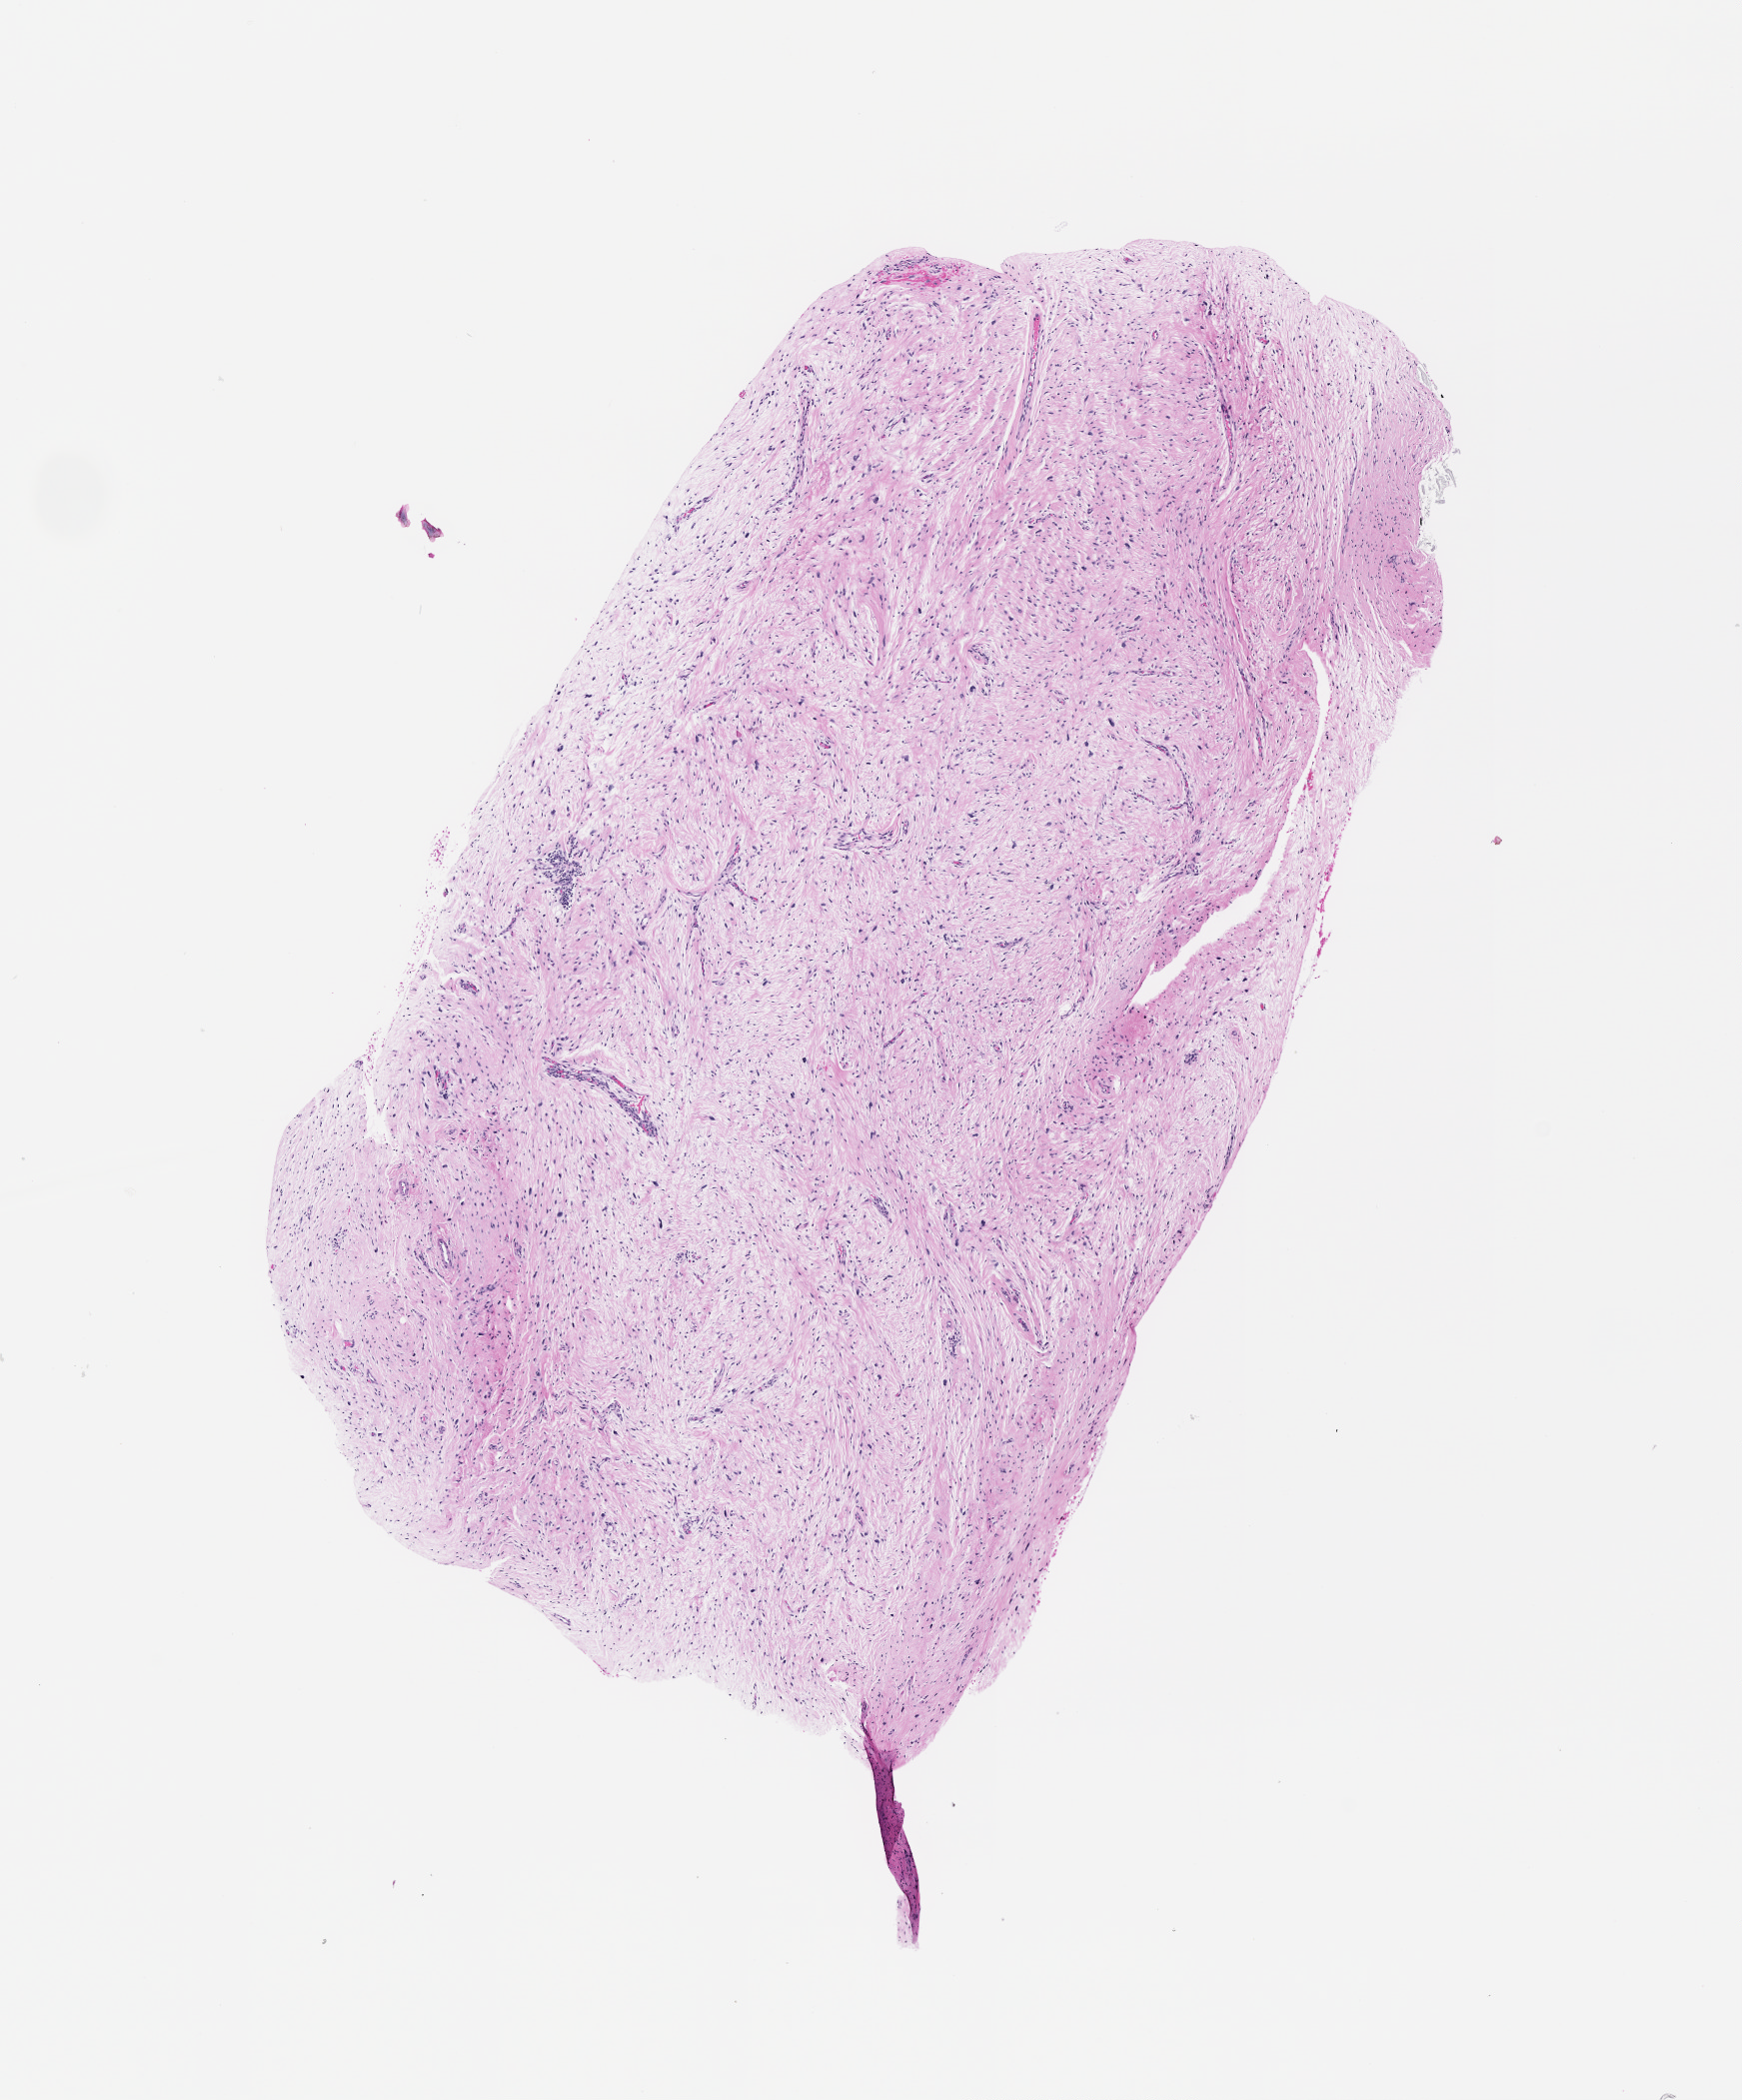
Digitized Hematoxylin and eosin (H&E) stained tissue section (whole slide), shown as a low-resolution overview of the whole scanned area (about 7.0 x 8.5 mm, acquisition: 20x scan).
Patient diagnosis (cohort enrolment): sarcoma (site not recorded at cohort level).